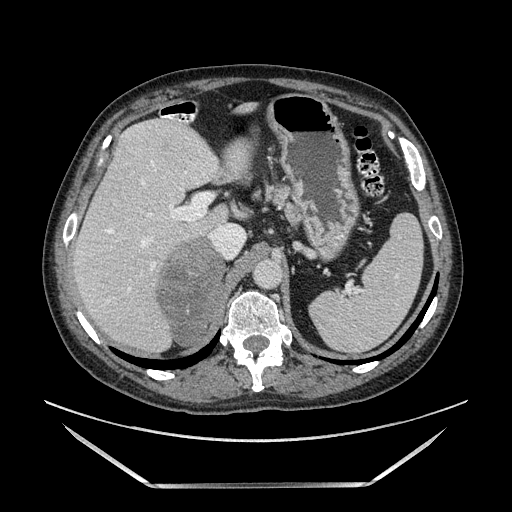
Contrast-enhanced abdominal CT, one axial slice. Slice 100 of 185 in the series (ordered by position). Soft-tissue window (W 400 / L 40 HU). 512 × 512 image matrix, field of view 440 × 440 mm. Male patient. Case-level facts recorded for this patient, not image findings: diagnosis: adrenocortical carcinoma; tumour side: right adrenal; tumour size at pathology: 10.3 cm.
Outlined on this slice (semi-automatic segmentation, software-assisted and operator-edited):
- mass: bounding box <160,236,225,342> (left, top, right, bottom; pixels)